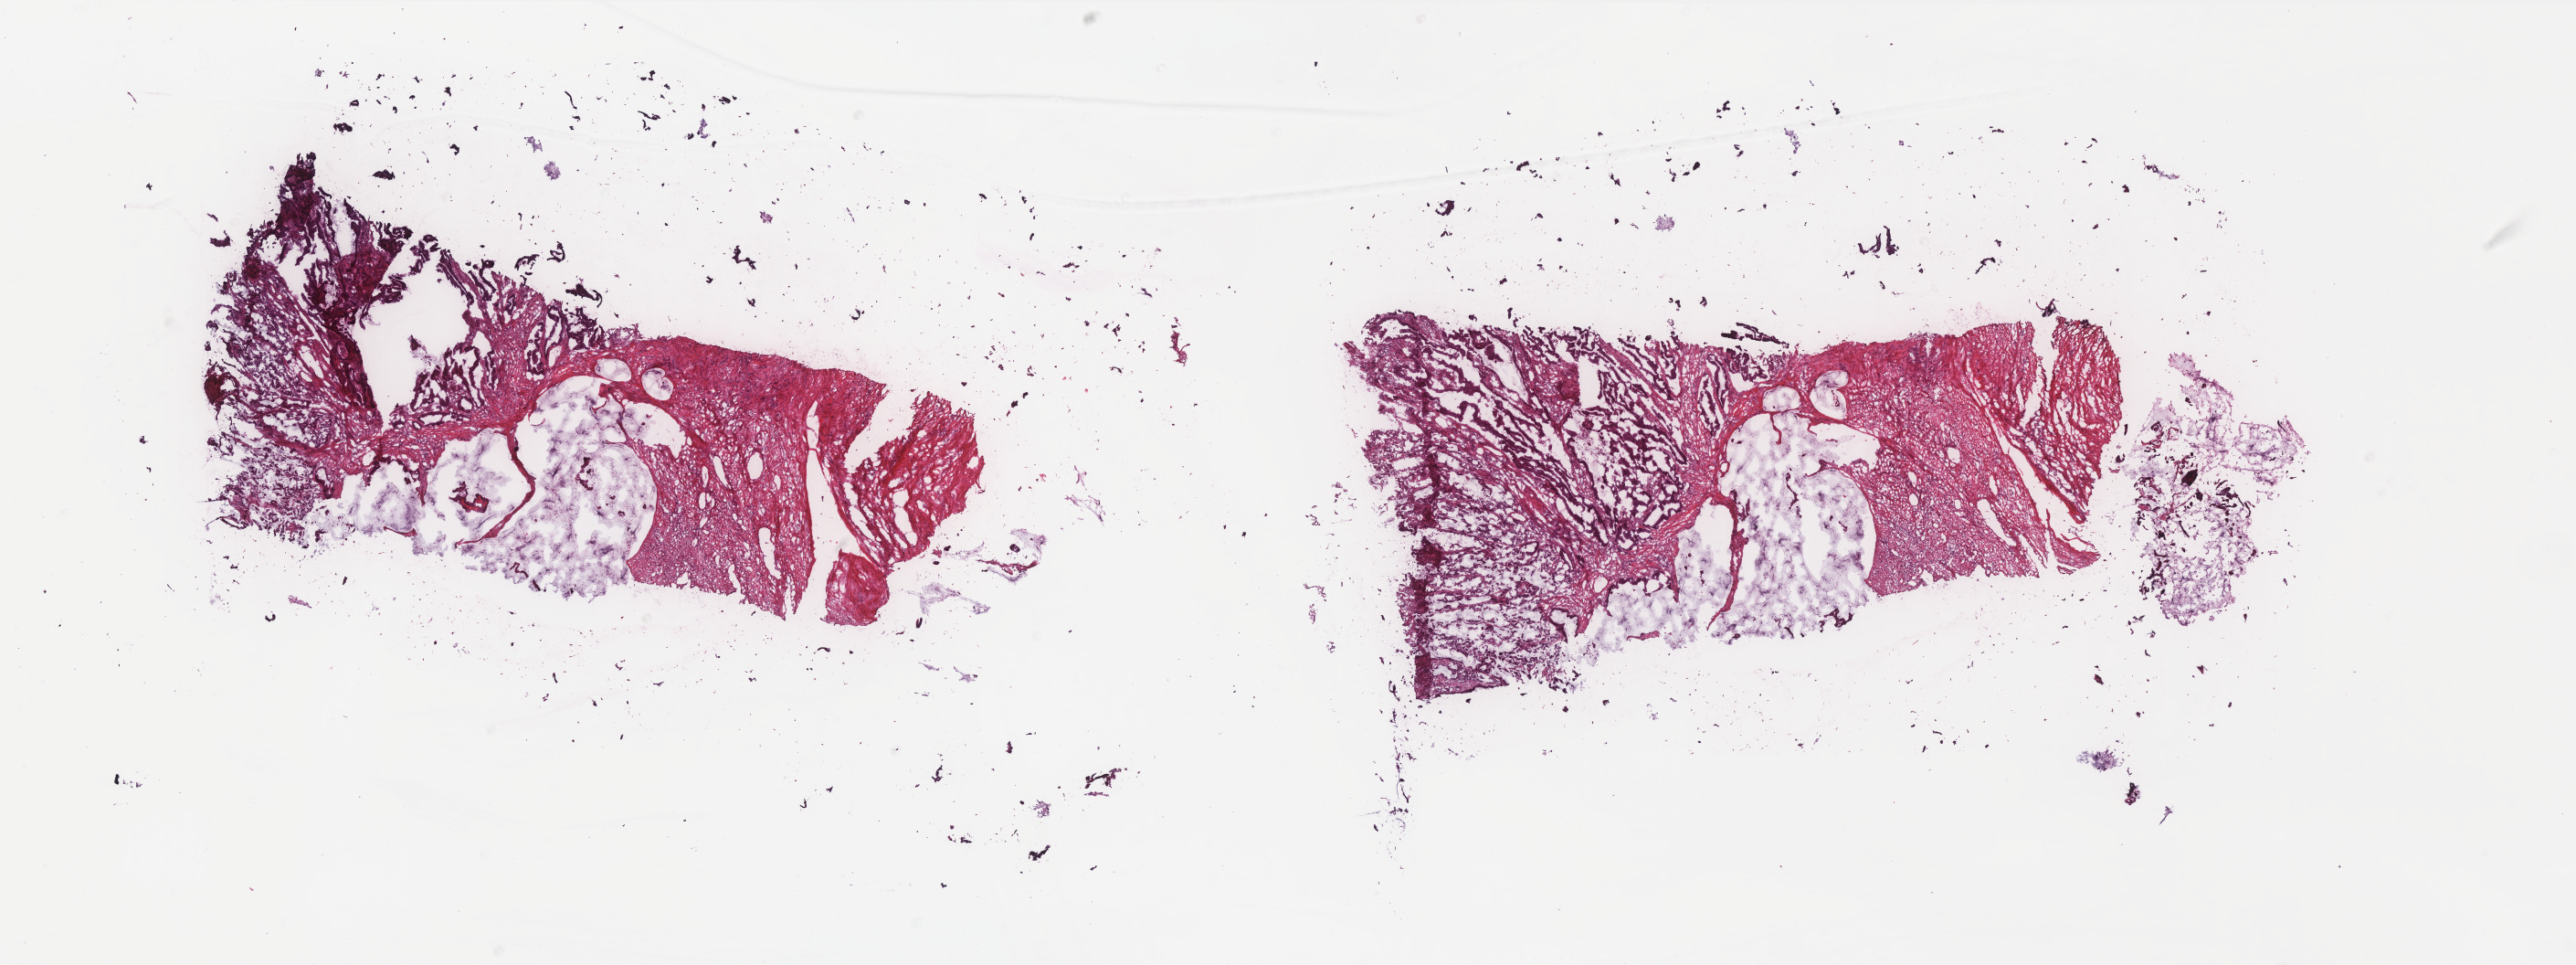
H&E whole-slide image — whole scanned area (about 22.6 x 8.5 mm, from a 40x scan) shown as a low-resolution overview; frozen section from the top of the tissue portion; colon, primary tumour sample. Male patient. Composition of this section per pathologist review: tumour cells 70%, tumour nuclei 60%, normal cells 0%, stromal cells 30%, necrosis 0%. Infiltration values recorded for this section: lymphocyte infiltration 0%, monocyte infiltration 0%, neutrophil infiltration 0%.
TNM: T3 N0 M0. AJCC pathologic stage: IIA. Lymph nodes positive (case pathology): 0 of 6 examined. Diagnosis: Mucinous adenocarcinoma (splenic flexure of colon).